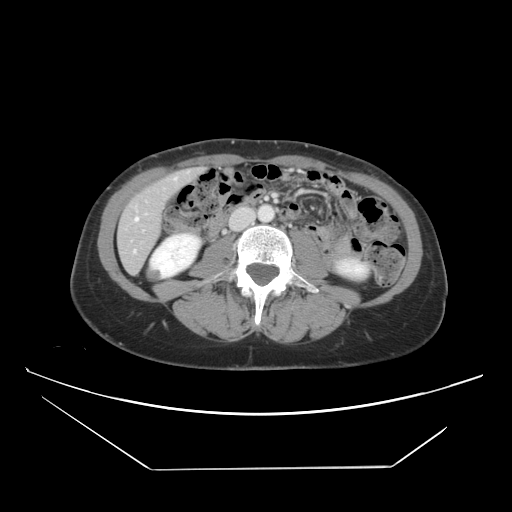
Contrast-enhanced abdominal CT, one axial slice; position 12 of 42 along the scan axis; intravenous contrast given; soft-tissue window (W 400 / L 40 HU); 5 mm slice thickness; 512 × 512 image matrix. Female patient, age 52 years. Case-level facts recorded for this patient, not image findings: diagnosis: colorectal cancer liver metastases, imaged before liver resection; multiple liver metastases: yes.
Structures marked on this image (expert manual segmentation):
- hepatic veins: bounding box (x1, y1, x2, y2) in pixels: (133, 171, 191, 252)
- liver: (119, 170, 197, 272)
- planned liver remnant (the part of the liver to remain after resection): (127, 170, 197, 218)
- portal vein (with intrahepatic branches): (265, 197, 268, 200)